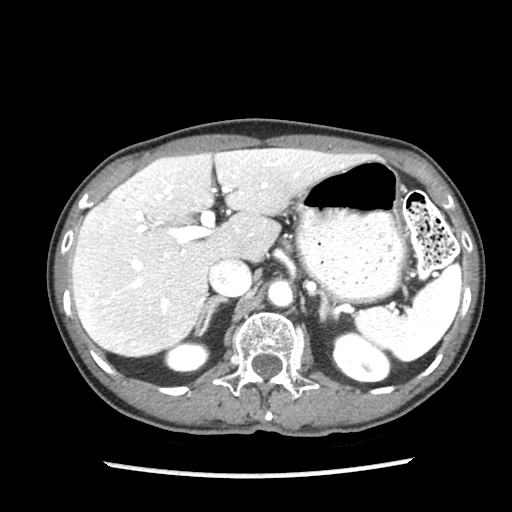
Contrast-enhanced abdominal CT (liver protocol), one axial slice. Position 56 of 87 along the scan axis. Reconstruction kernel STANDARD. 140 kVp. Soft-tissue window (W 400 / L 40 HU). 512 × 512 image matrix, field of view 300 × 300 mm. Case-level facts recorded for this patient, not image findings: diagnosis: hepatocellular carcinoma (patient treated with transarterial chemoembolisation; whether this scan precedes or follows treatment is not stated here); TNM stage (as recorded): Stage-IIIB; Child-Pugh class: A; tumour differentiation: well differentiated; tumour nodularity: uninodular.
Annotated regions visible in this slice (semi-automatically segmented with operator editing):
- liver parenchyma outside the tumour (the mass and vessels are separate outlines, so this box may not span the whole liver): bounding box [x1, y1, x2, y2] px = [72, 148, 365, 356]
- liver vessels: [85, 160, 298, 329]